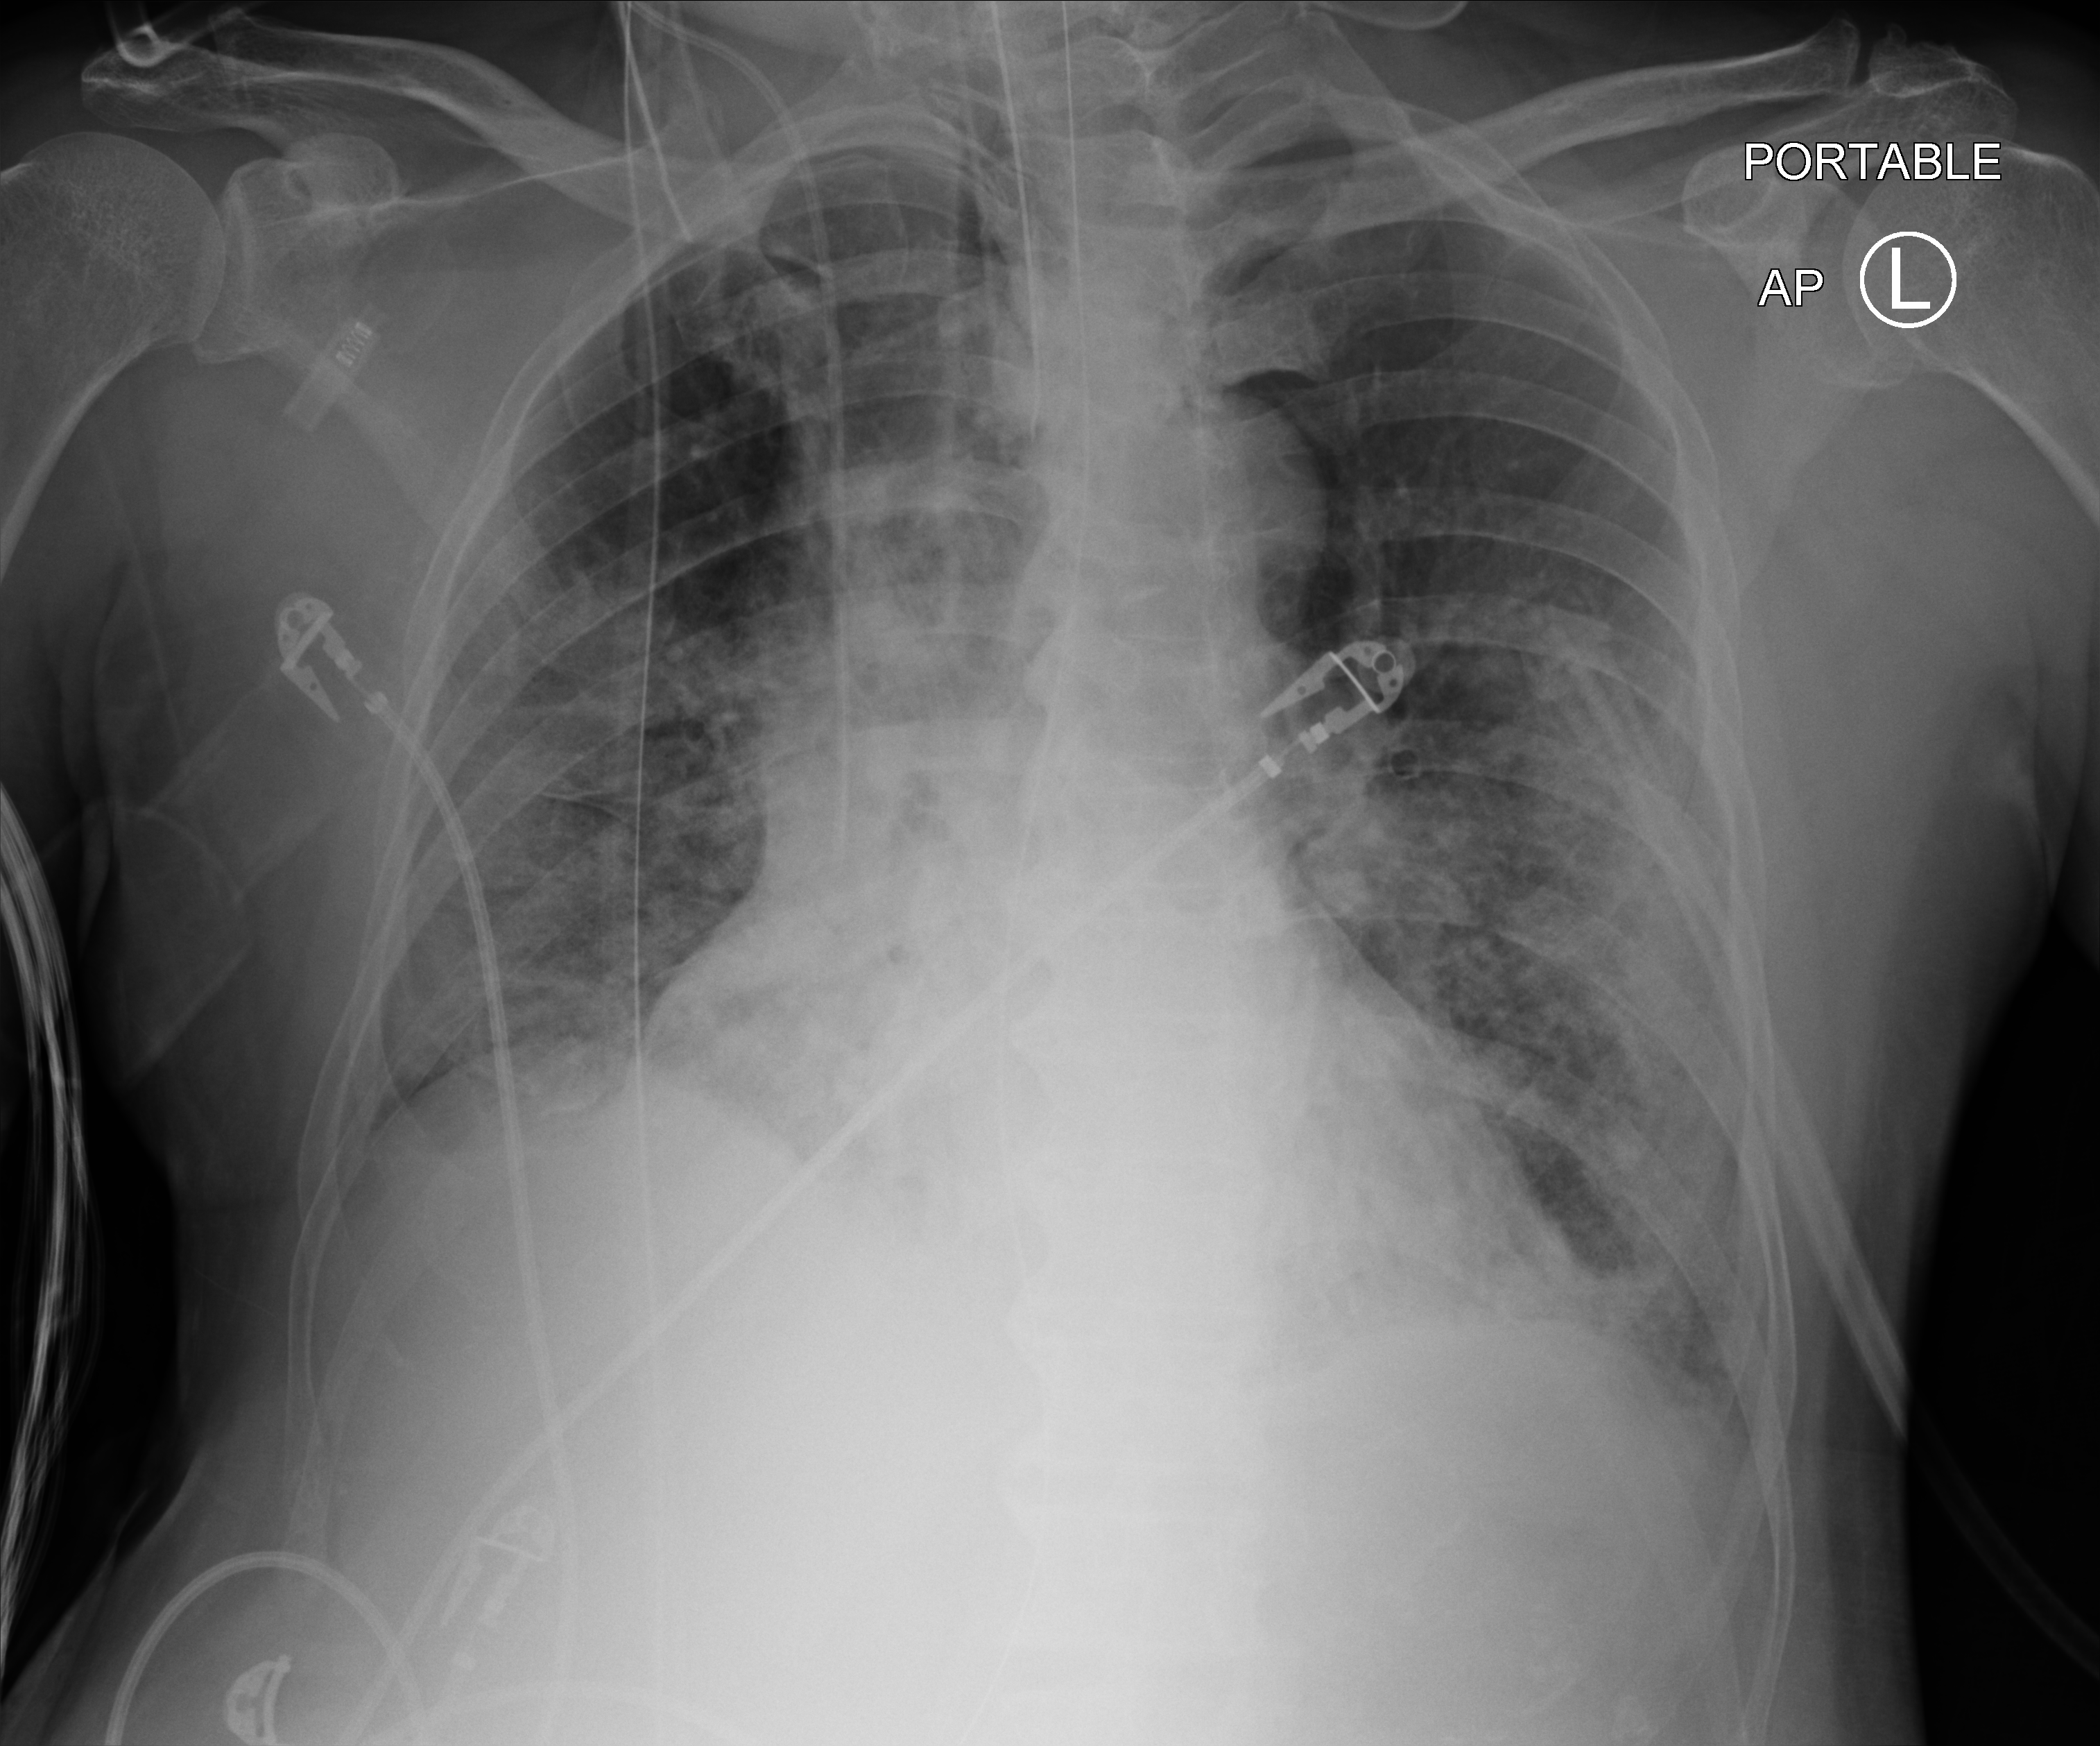
Portable chest radiograph, anteroposterior (AP) projection. Male patient hospitalised with COVID-19, age 60–74 years.
Admission-level facts for this patient (not findings on this image; timing relative to this image not recorded):
- admitted to intensive care during this hospital stay: yes
- mechanically ventilated during this hospital stay: yes
- hypertension (admission record): yes